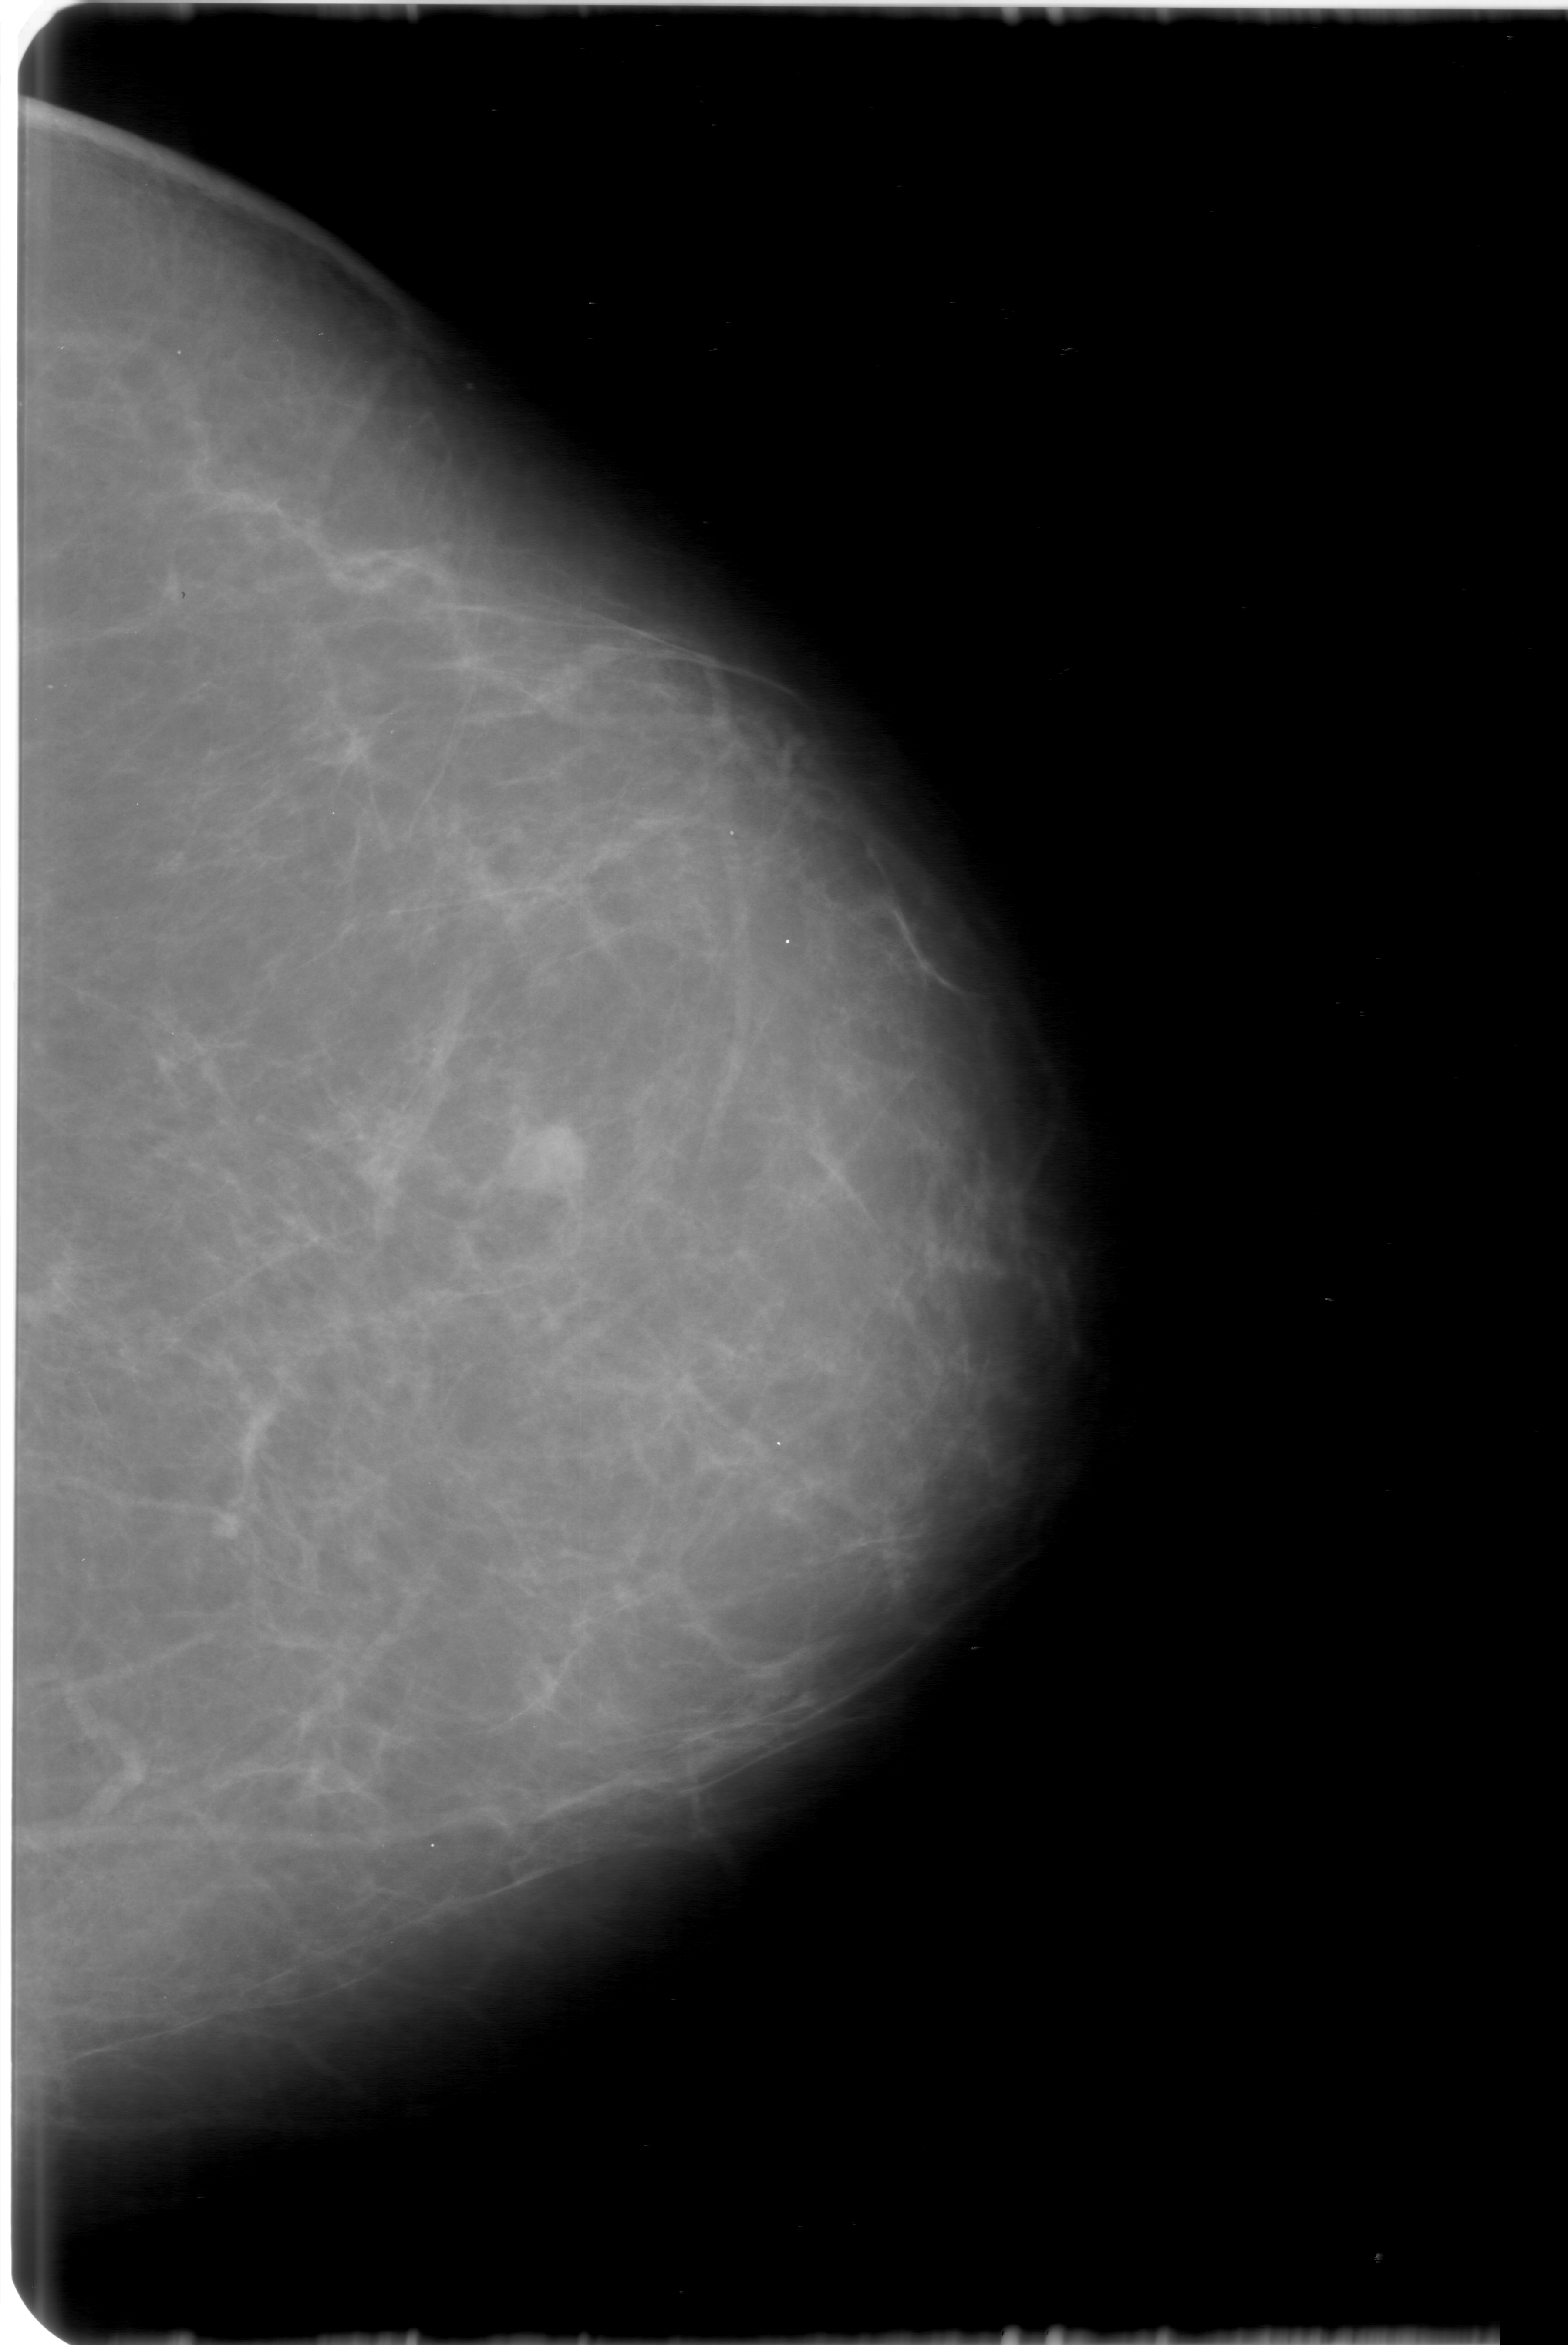
Scanned film-screen mammogram, left breast, craniocaudal (CC) view.
Mass, shape oval, margins obscured; BI-RADS assessment category 3; subtlety rating 4 on a 1 (subtle) to 5 (obvious) scale; pathology (as recorded): malignant.